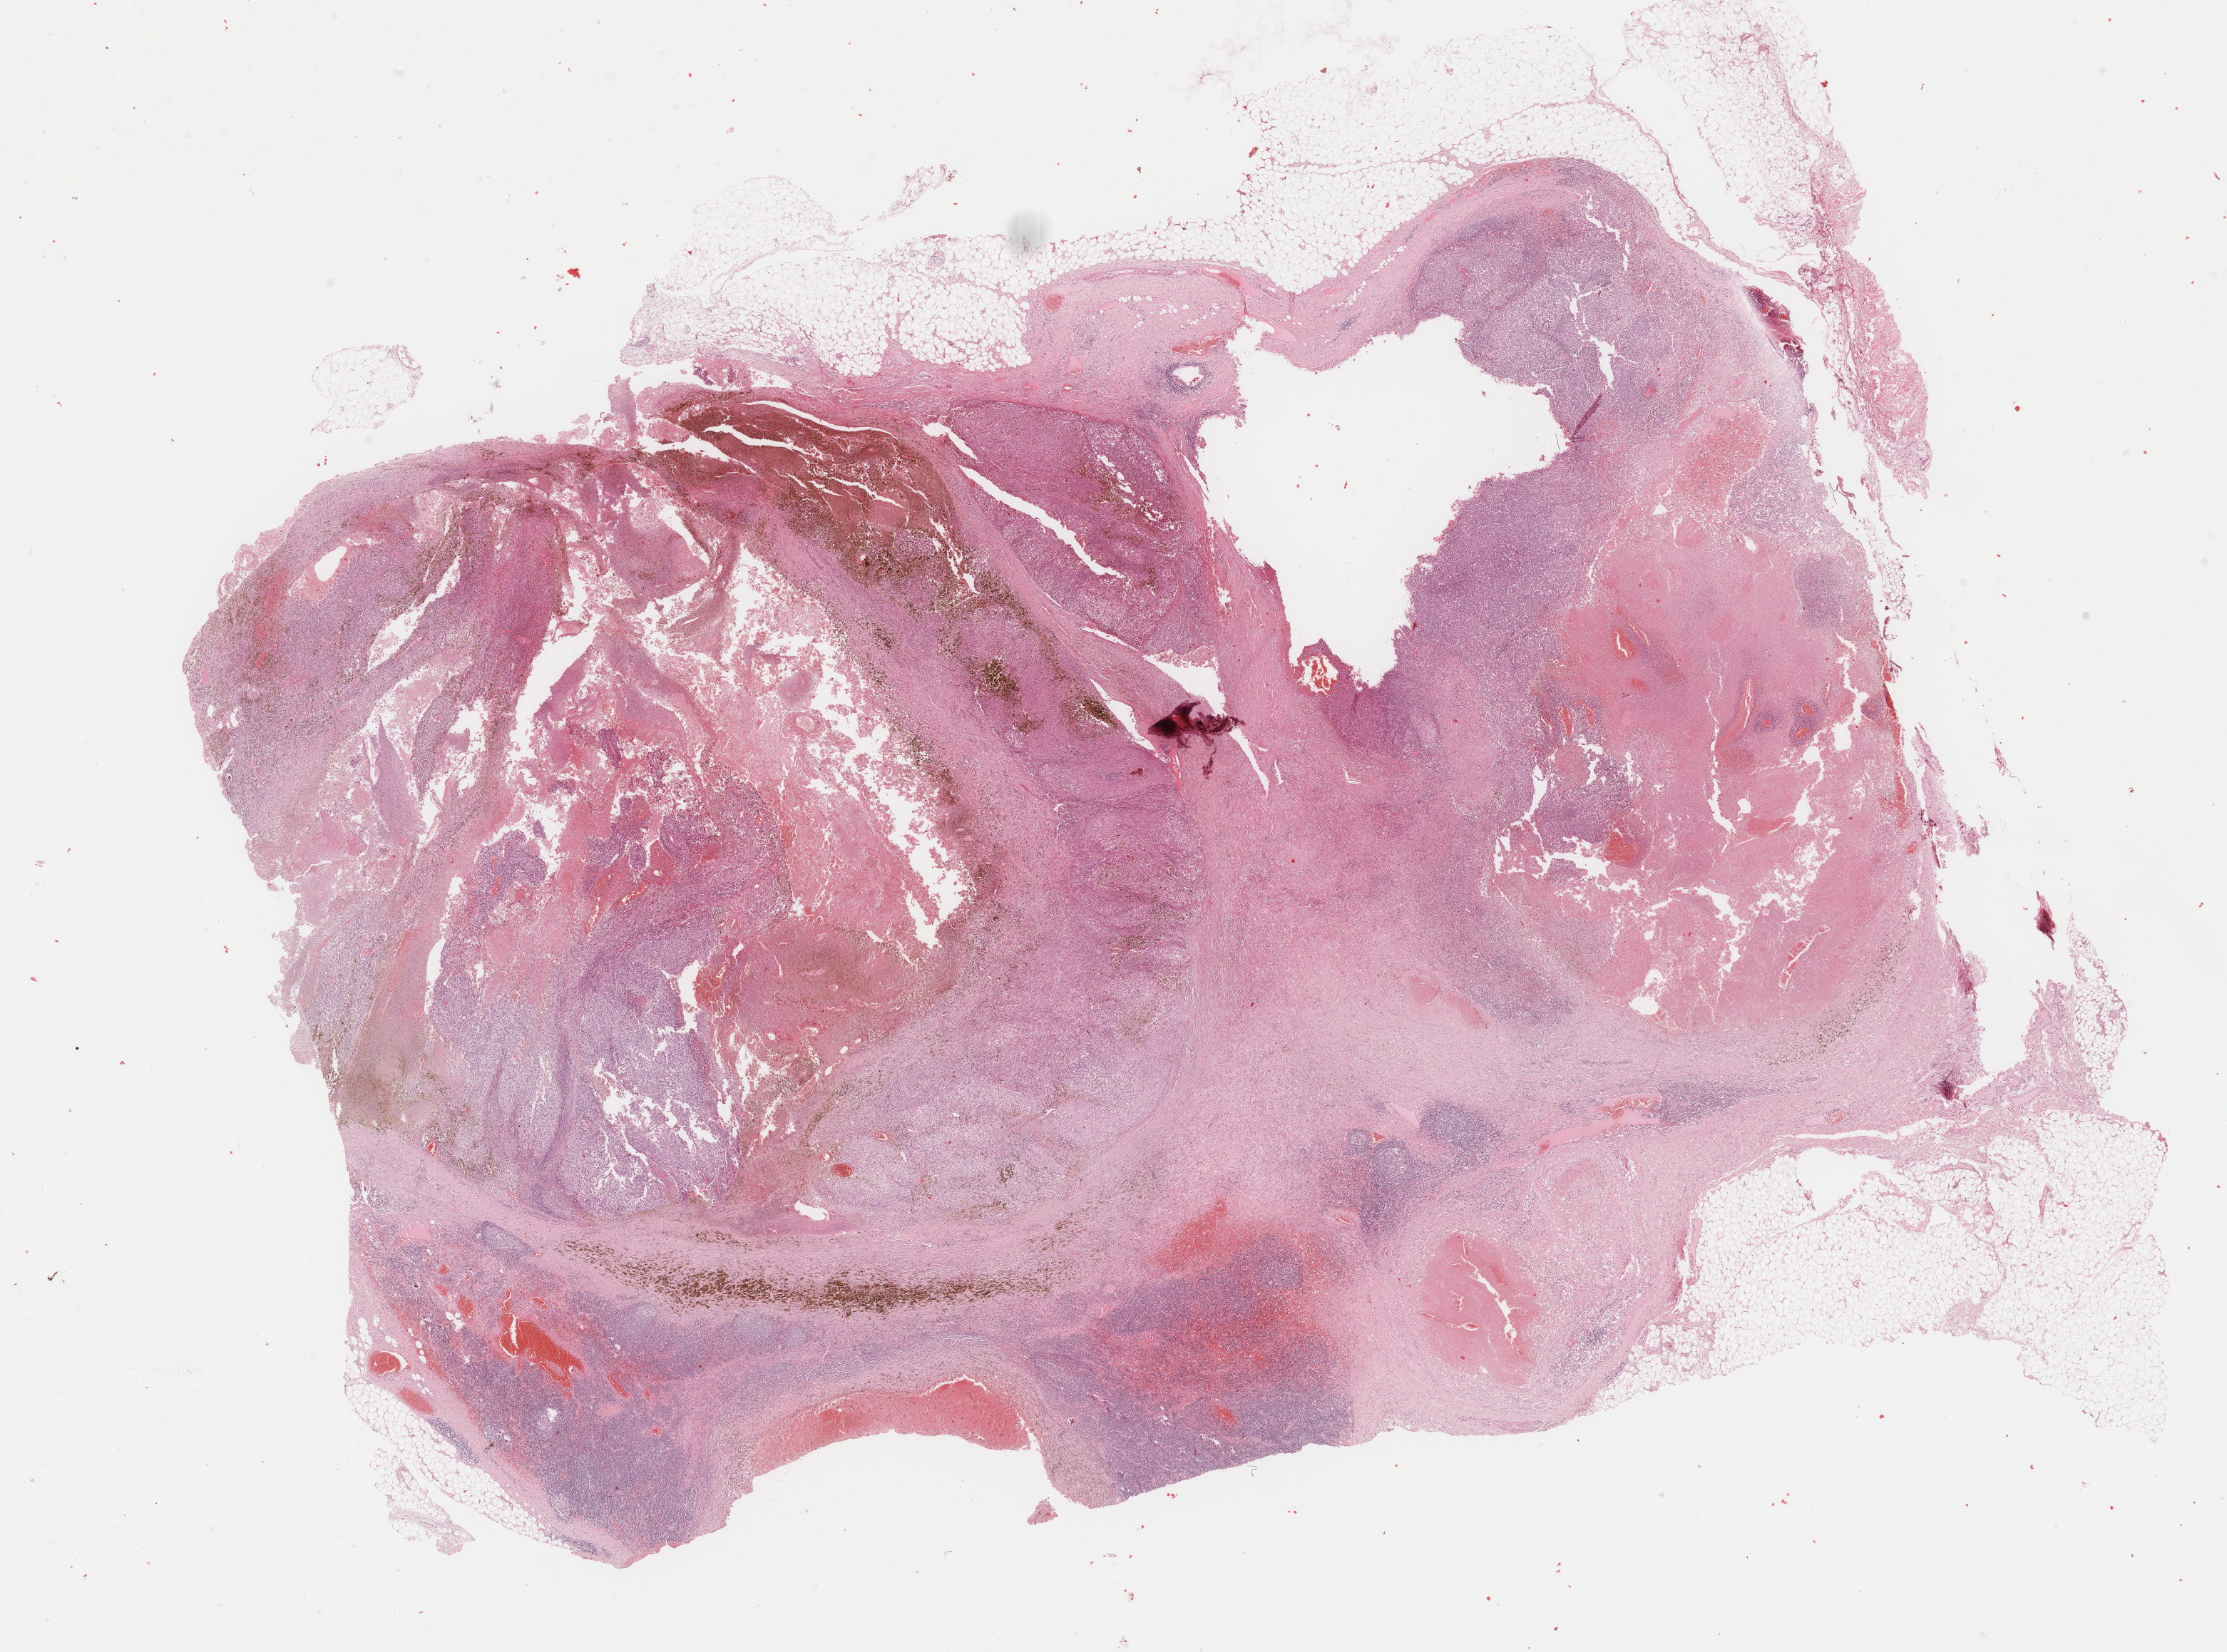
Digitized H&E tissue section (whole slide), low-resolution overview of the scanned area, about 24.8 x 18.4 mm; formalin-fixed paraffin-embedded (FFPE) diagnostic section; metastatic tumour sample, sampled site not recorded. Female patient; age at initial diagnosis 80 years.
This section: metastatic tumour tissue. Patient diagnosis: Malignant melanoma, NOS.